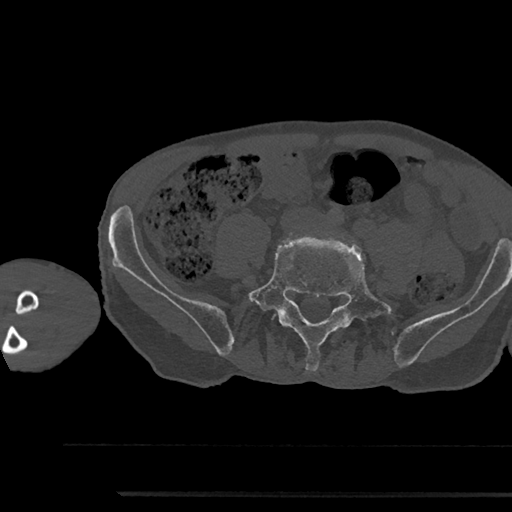
CT including the spine, one axial slice. Position 352 of 797 along the scan axis. Reconstruction kernel Br40s/3. Bone window (W 1800 / L 400 HU). 512 × 512 image matrix, field of view 367 × 367 mm. Male patient, age 79 years. From the clinical record (not read from this slice): primary cancer: prostate.
Structures marked on this image (semi-automatically segmented with operator editing):
- L5 vertebra: box from (x=243, y=237) to (x=396, y=371) px